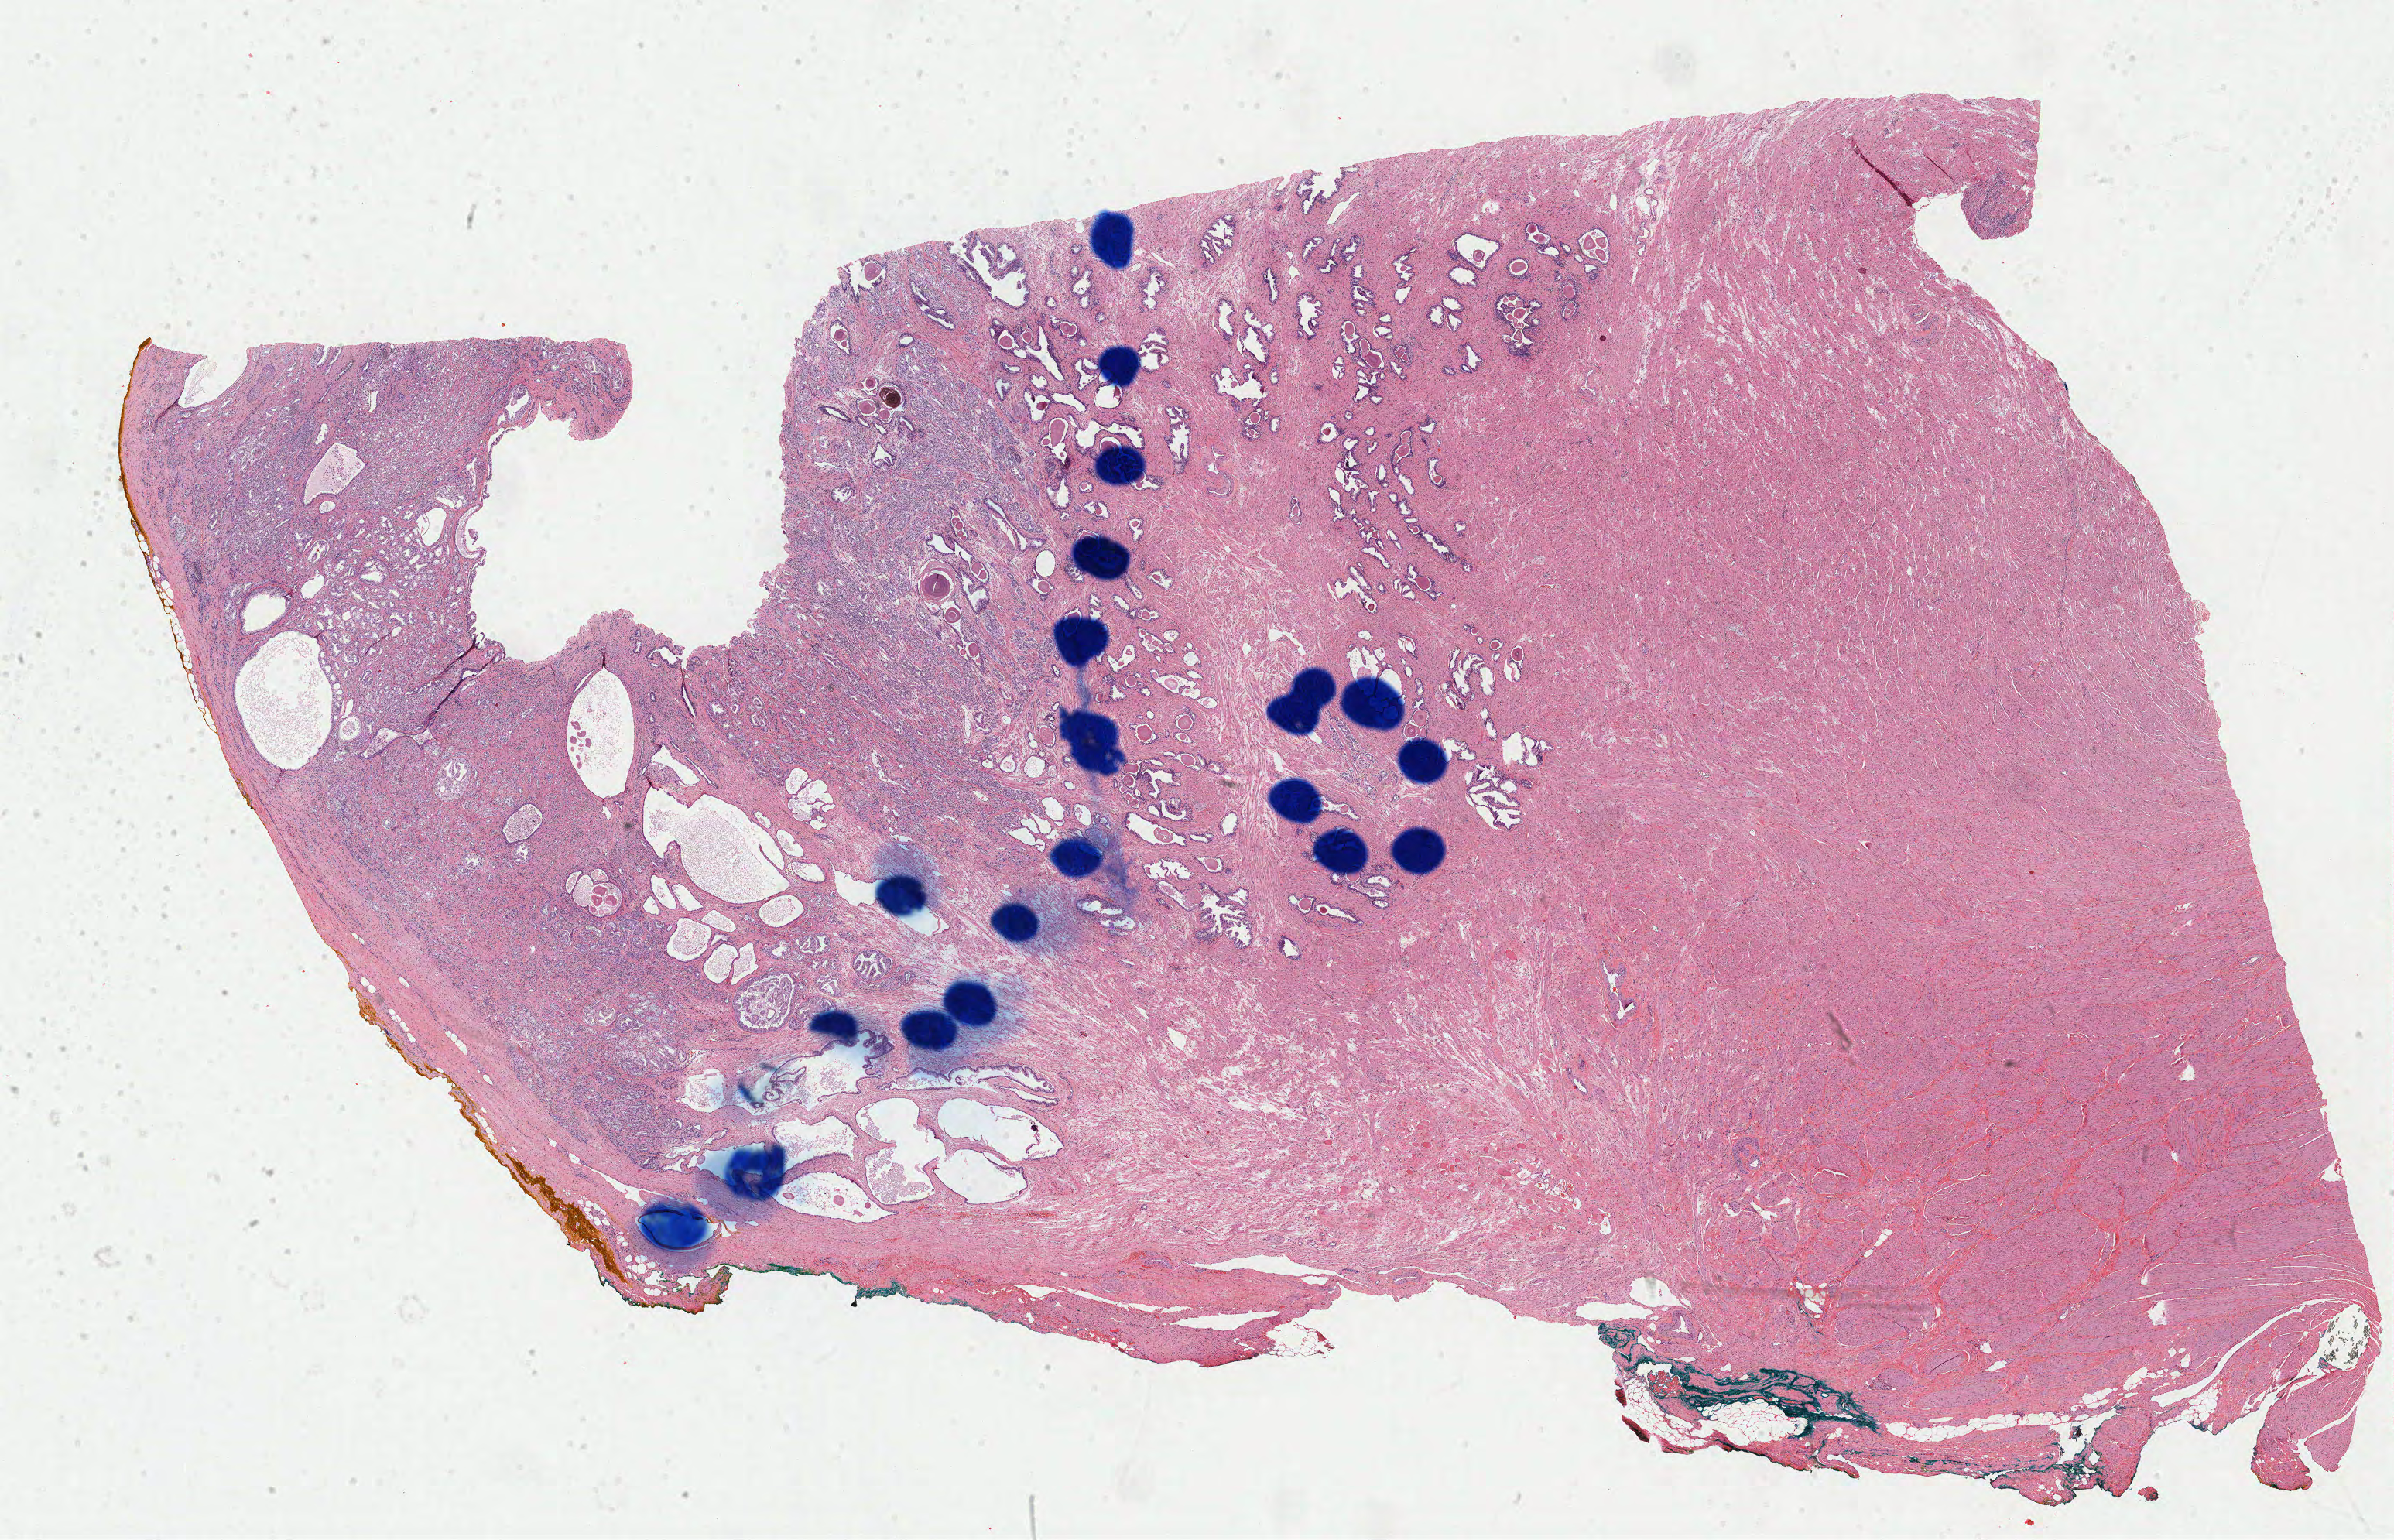
Digitized H&E tissue section (whole slide) — shown as a low-resolution overview of the whole scanned area (about 24.6 x 15.8 mm, slide scanned at 40x). Formalin-fixed paraffin-embedded (FFPE) diagnostic section. Prostate, primary tumour sample. Patient: male, age at initial diagnosis 59 years. Gleason score: 7 (4+3).
Lymph nodes positive (case pathology): 1 of 34 examined. Laterality: bilateral. Histologic diagnosis: Adenocarcinoma, NOS (prostate gland).